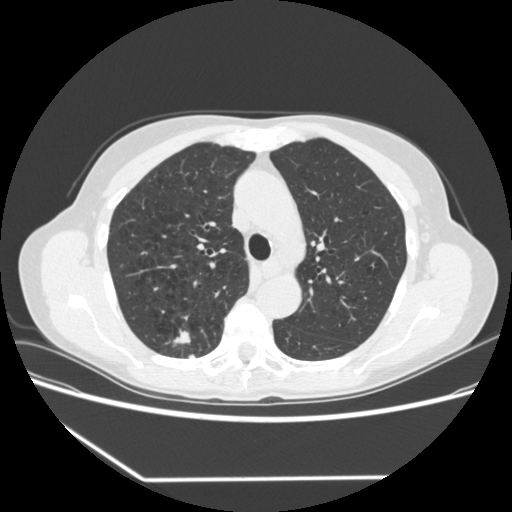
Low-dose screening chest CT, one axial slice; slice 236 of 323 in the series (ordered by position); reconstruction kernel STANDARD; 120 kVp; lung window (W 1500 / L -600 HU); 1.25 mm slice thickness; 512 × 512 image matrix, field of view 360 × 360 mm.
Annotated regions visible in this slice (outlined manually by an expert reader):
- lesion 1 (tumor, upper lobe of right lung): bounding box [x1, y1, x2, y2] px = [173, 329, 191, 346]